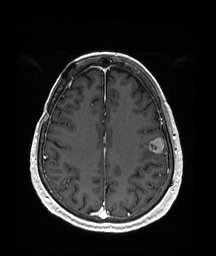
Brain MRI from a brain-tumour surgery series, one axial slice. Position 67 of 176 along the scan axis. T1-weighted post-contrast. 1 mm slice thickness. 216 × 256 image matrix, field of view 211 × 250 mm. From the clinical record (not read from this slice): histopathology: Metastatic Malignant Melanoma.
Structures marked on this image (manually delineated by an expert):
- tumour: box from (x=148, y=138) to (x=165, y=153) px